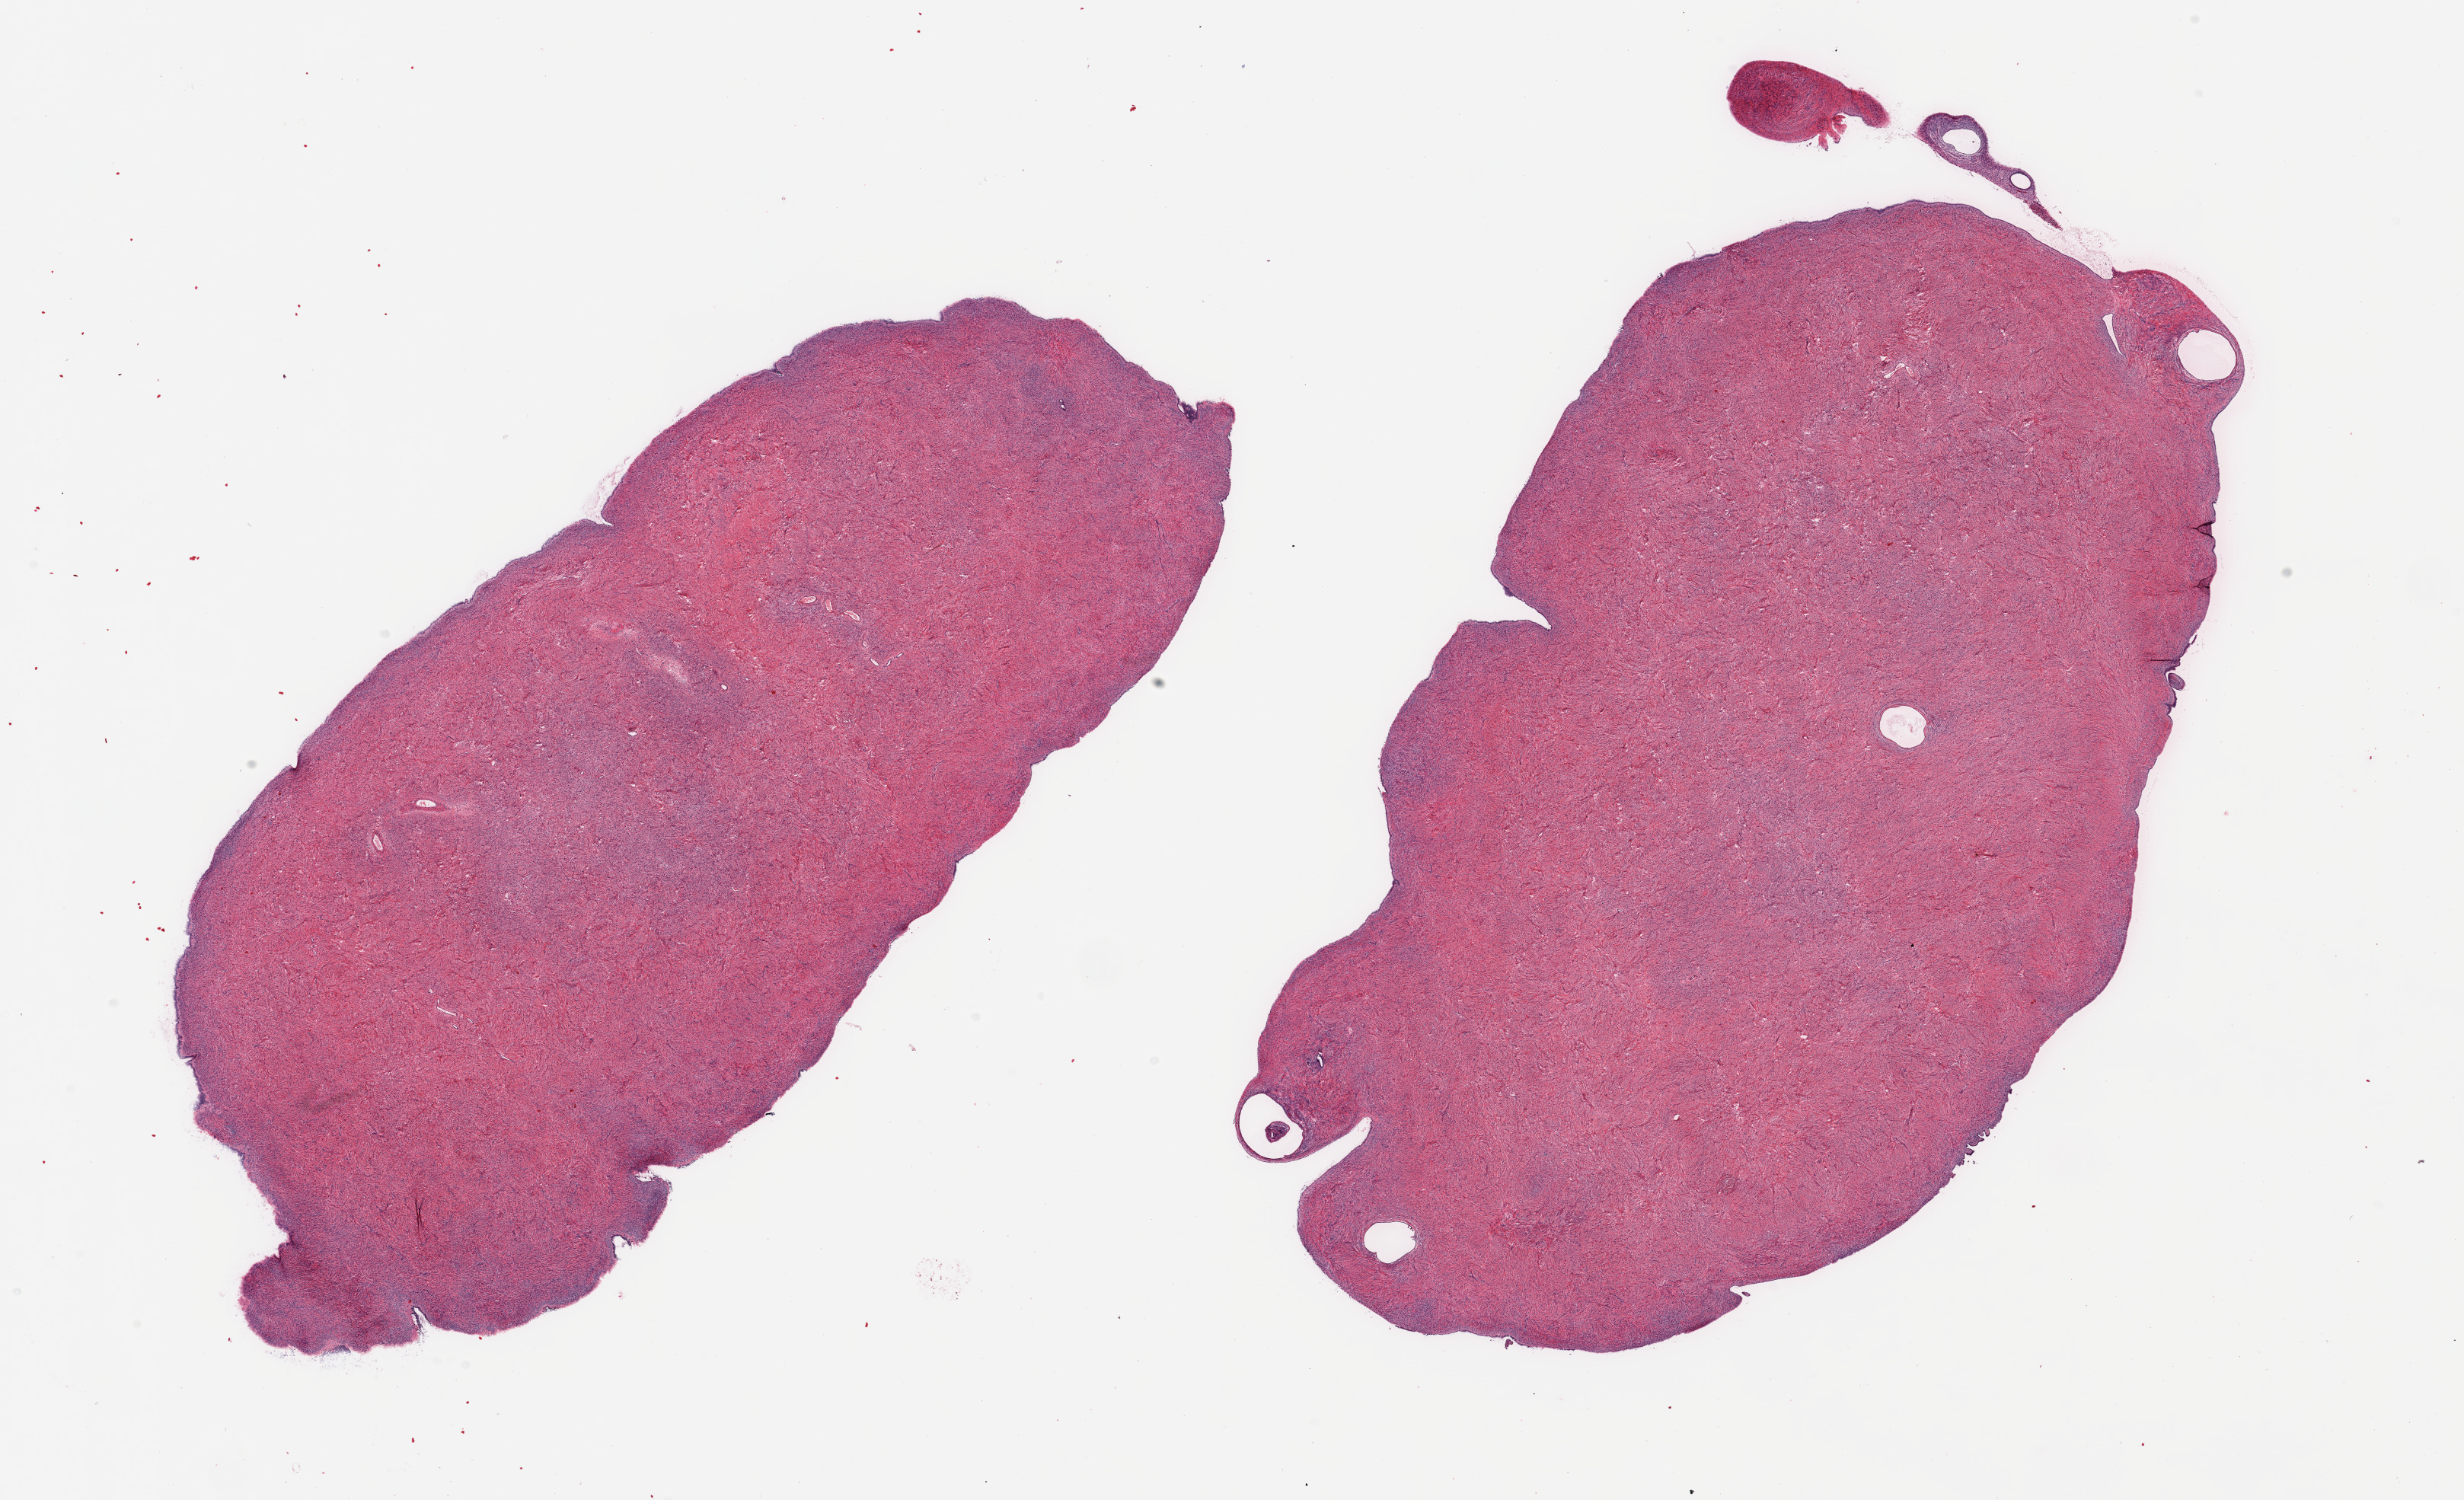
Hematoxylin and eosin (H&E) whole-slide image — low-resolution overview of the scanned area, about 25.6 x 15.6 mm (slide scanned at 20x). PAXgene-fixed paraffin-embedded (PFPE) section. Target tissue: ovary. Tissue donor sample. Donor sex: female.
Pathologist's review note for this sample: 2 pieces; few inclusion cysts.